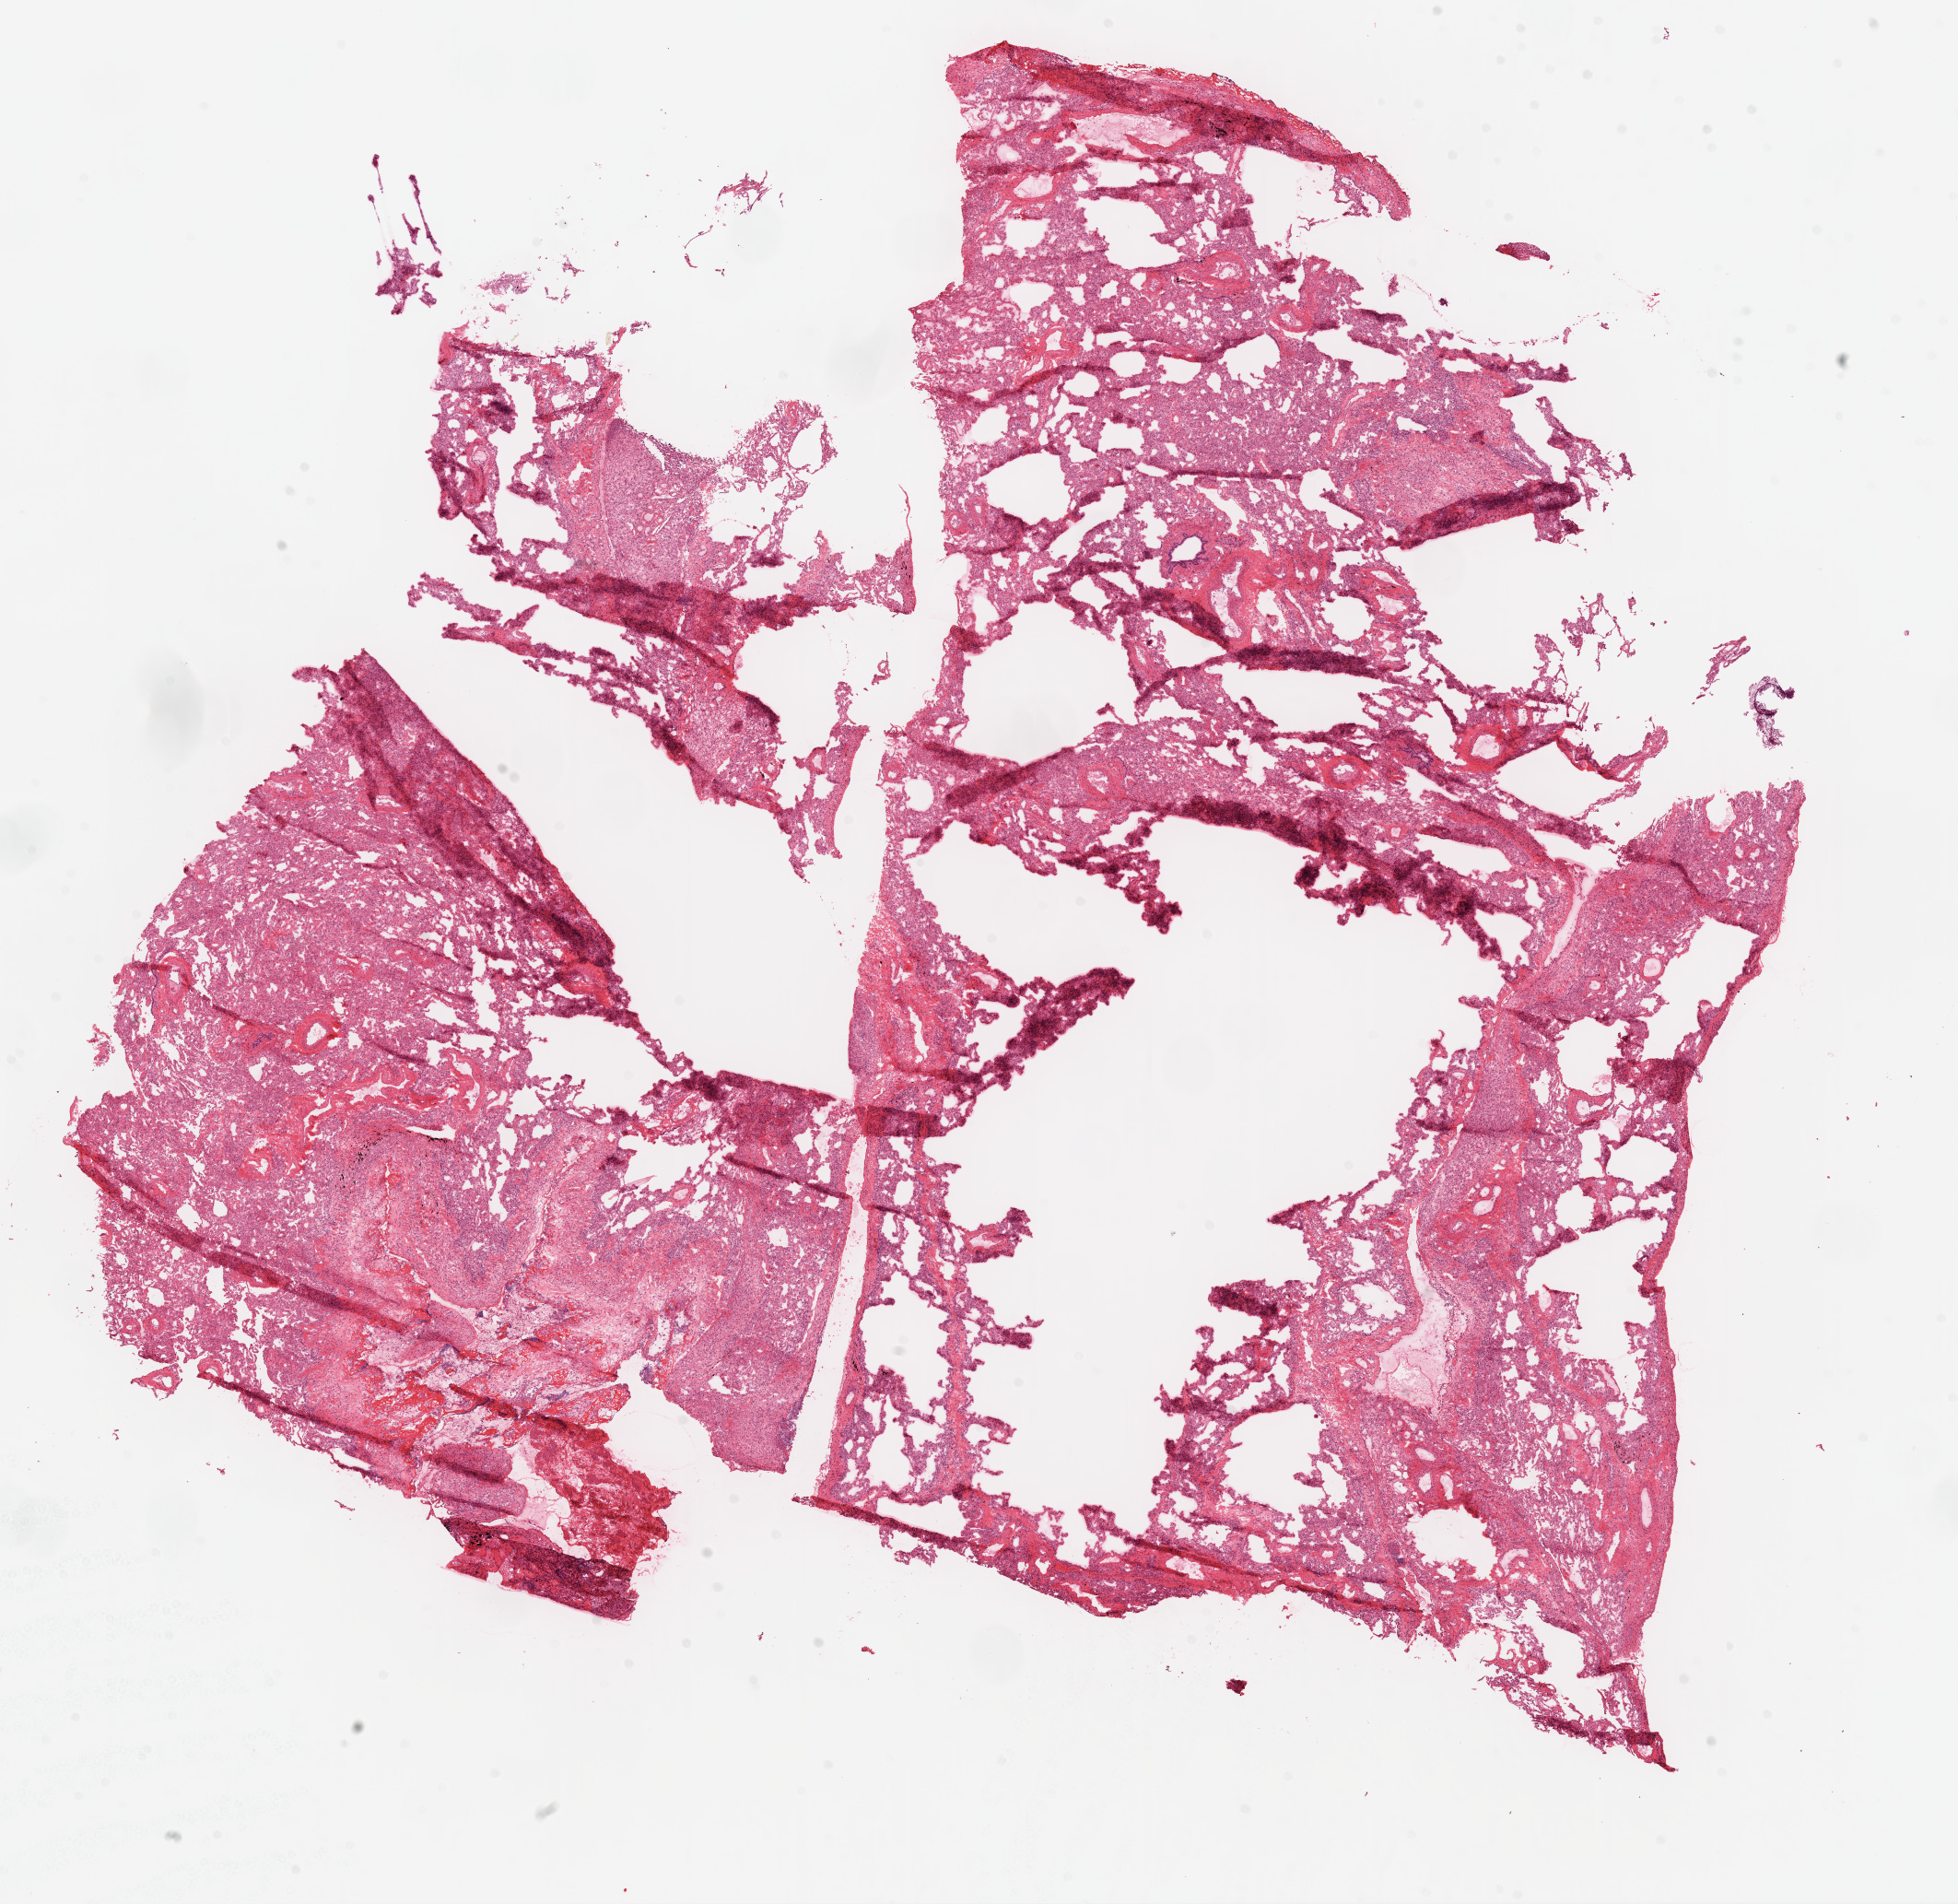
Whole-slide histology image, H&E-stained — whole scanned area (about 17.1 x 16.6 mm, slide scanned at 20x) shown as a low-resolution overview; frozen section from the top of the tissue portion; solid tissue normal (non-tumour tissue) sample from the lung. Male, age 67 years at initial diagnosis.
• this section: solid tissue normal (non-tumour) sample from the same patient
• patient diagnosis: Squamous cell carcinoma, NOS (lower lobe, lung)